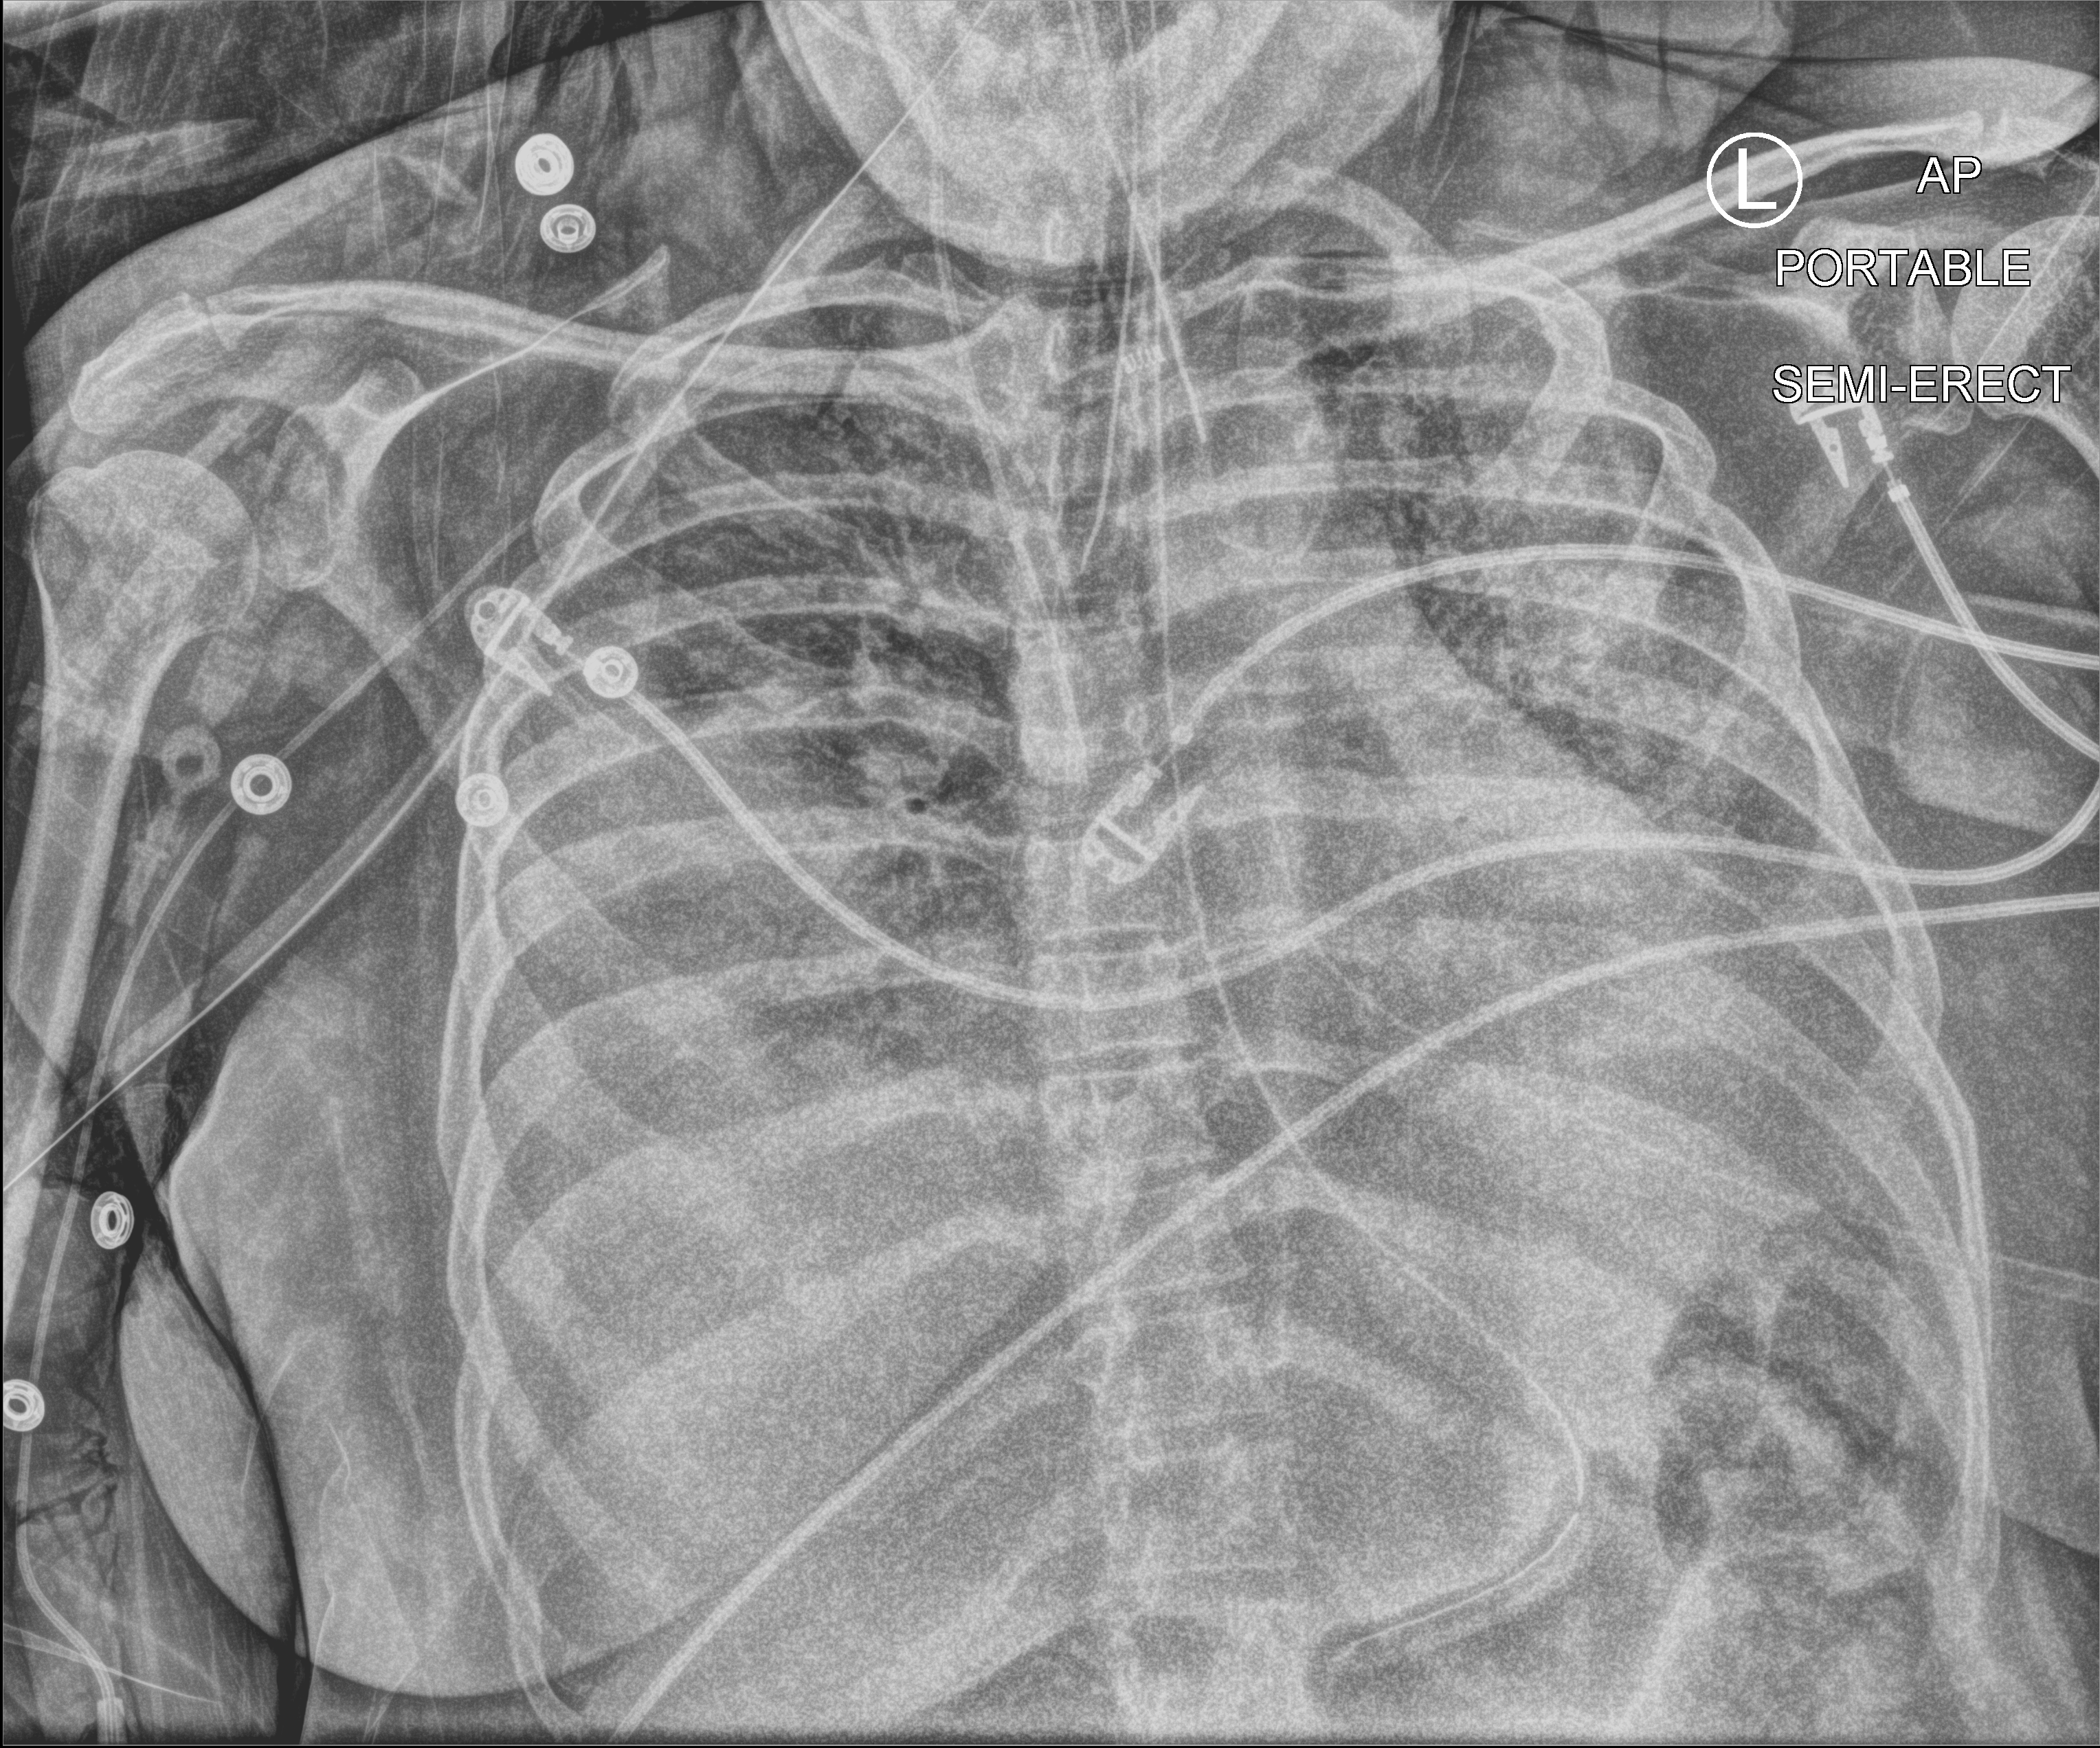
Chest X-ray (portable). Patient hospitalised with COVID-19, aged 18–59 years.
From the hospital-stay record, not from the radiograph (when in the stay this image was taken is not recorded):
- mechanically ventilated during this hospital stay: yes
- smoking status (admission record): never